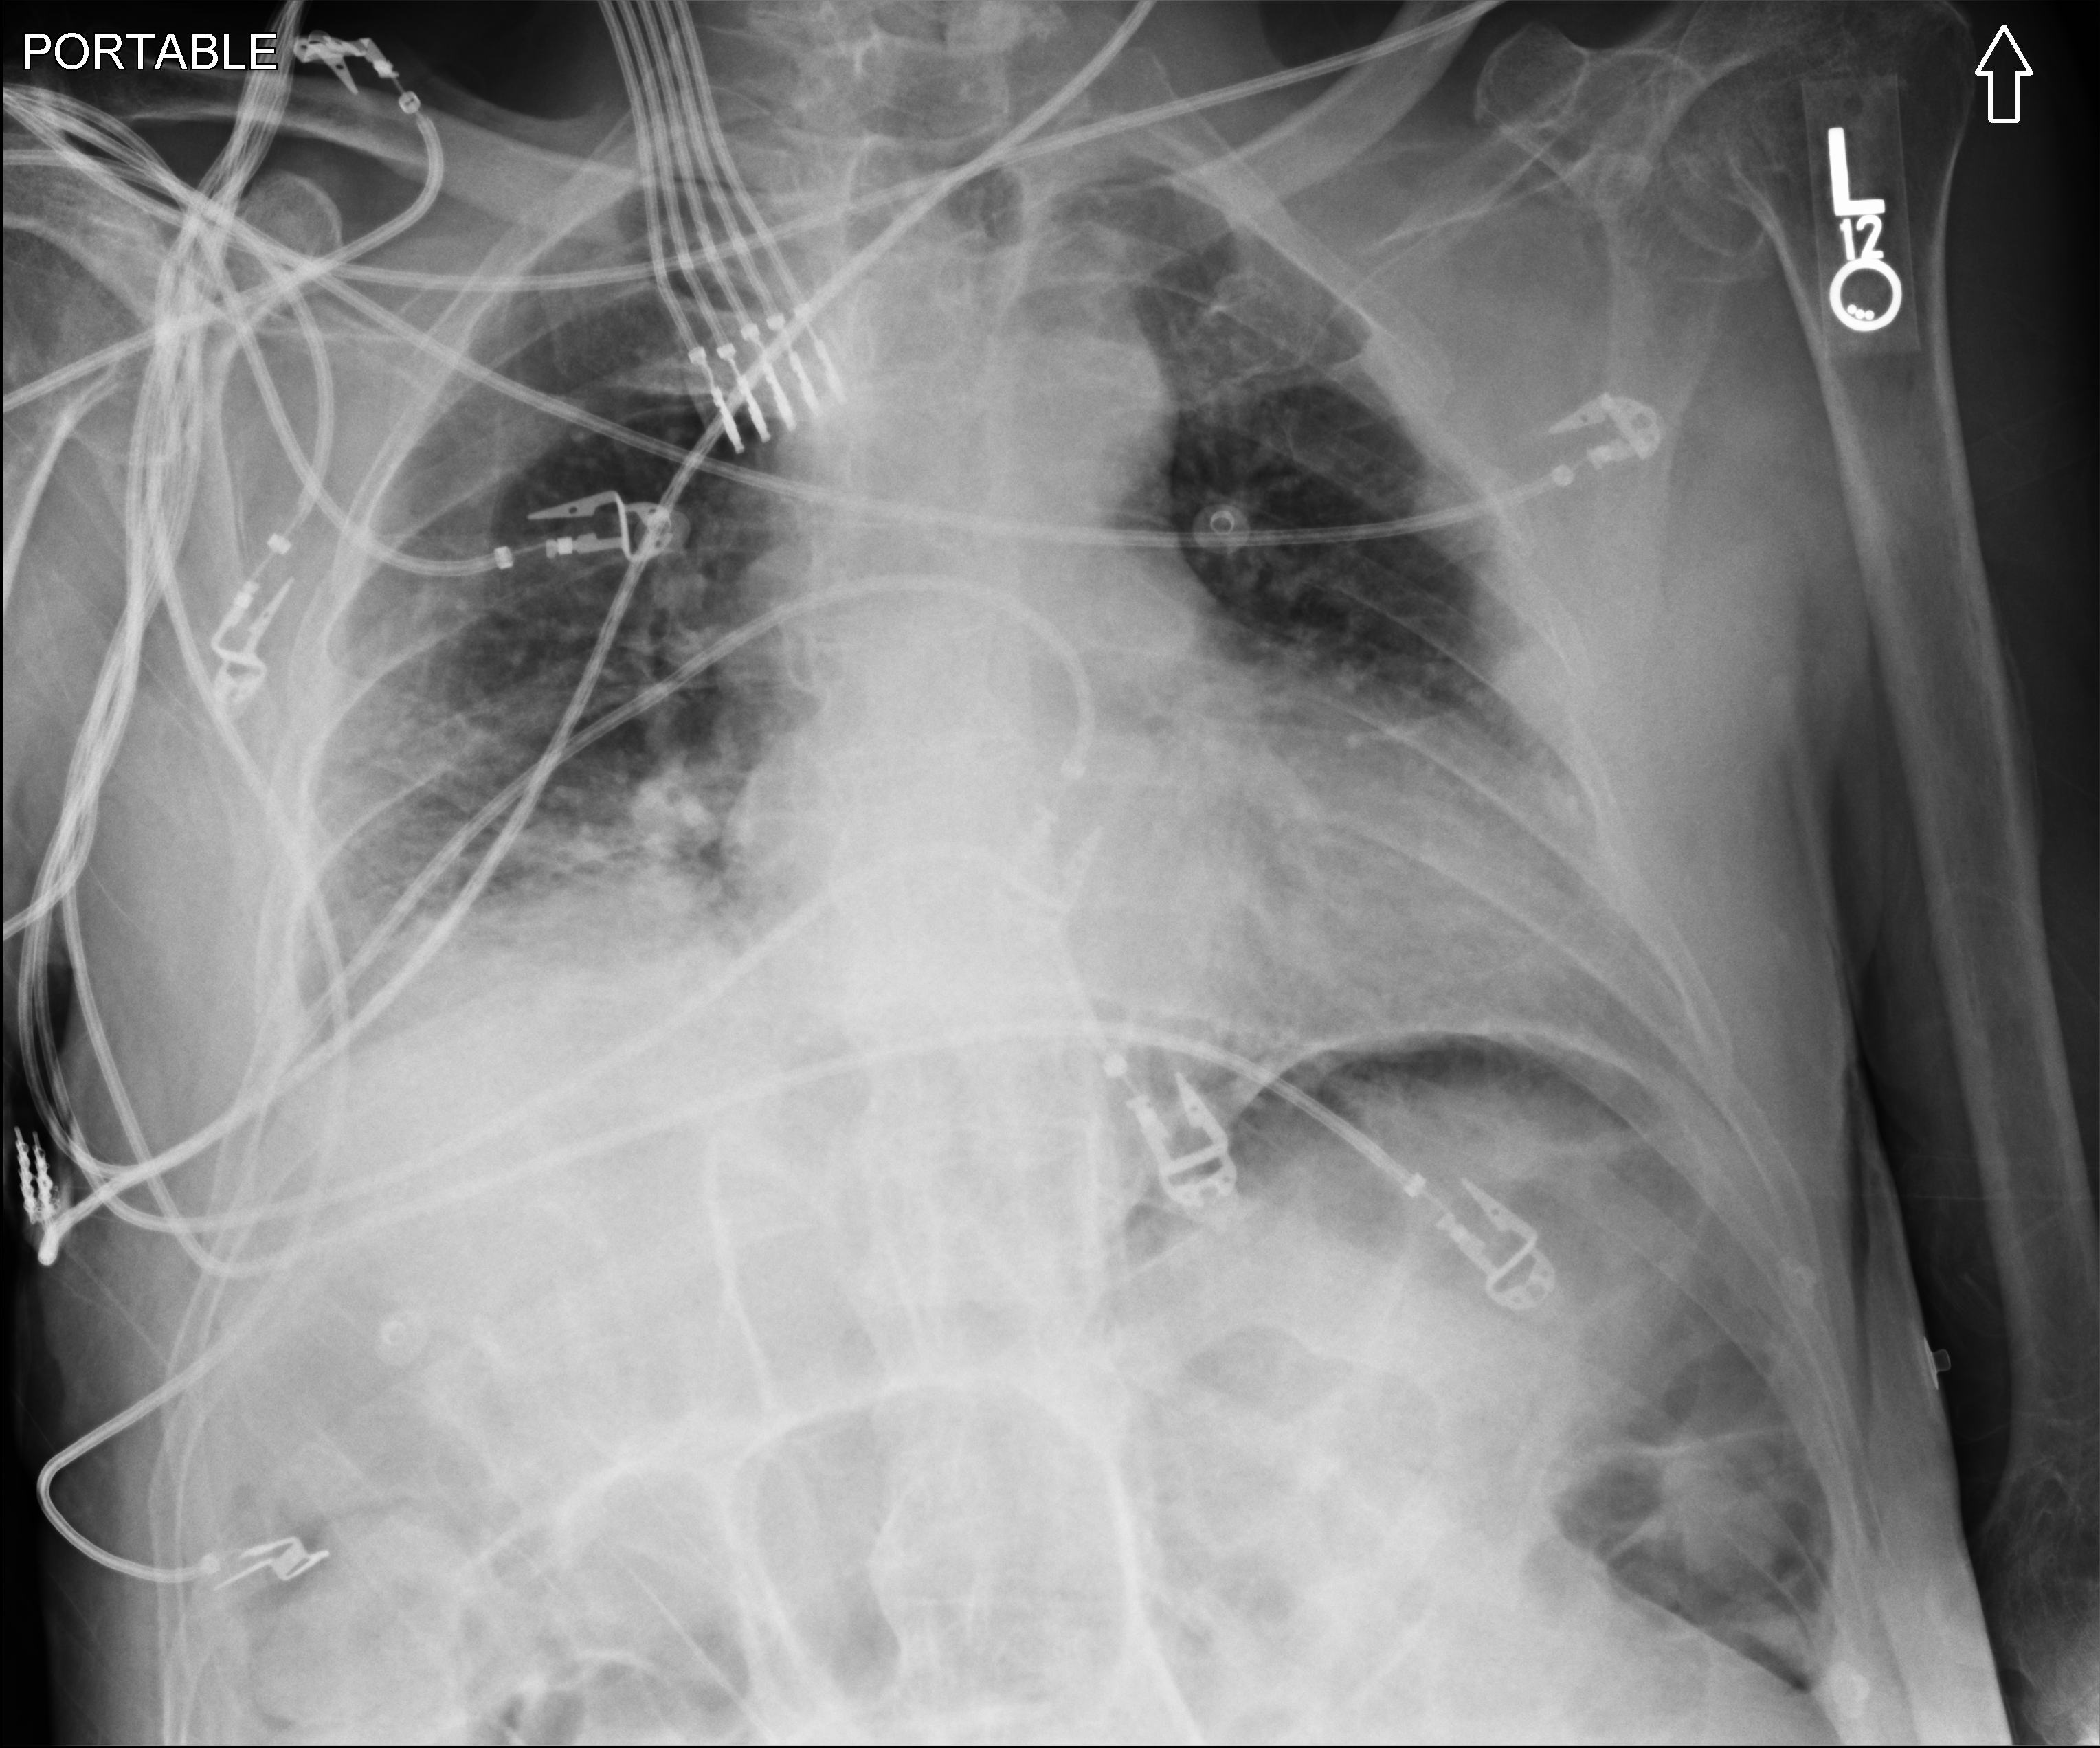
Portable chest radiograph, anteroposterior (AP) projection. Patient hospitalised with COVID-19; male, aged 75–90 years.
Admission-level facts for this patient (not findings on this image; timing relative to this image not recorded):
- length of hospital stay: 1 day